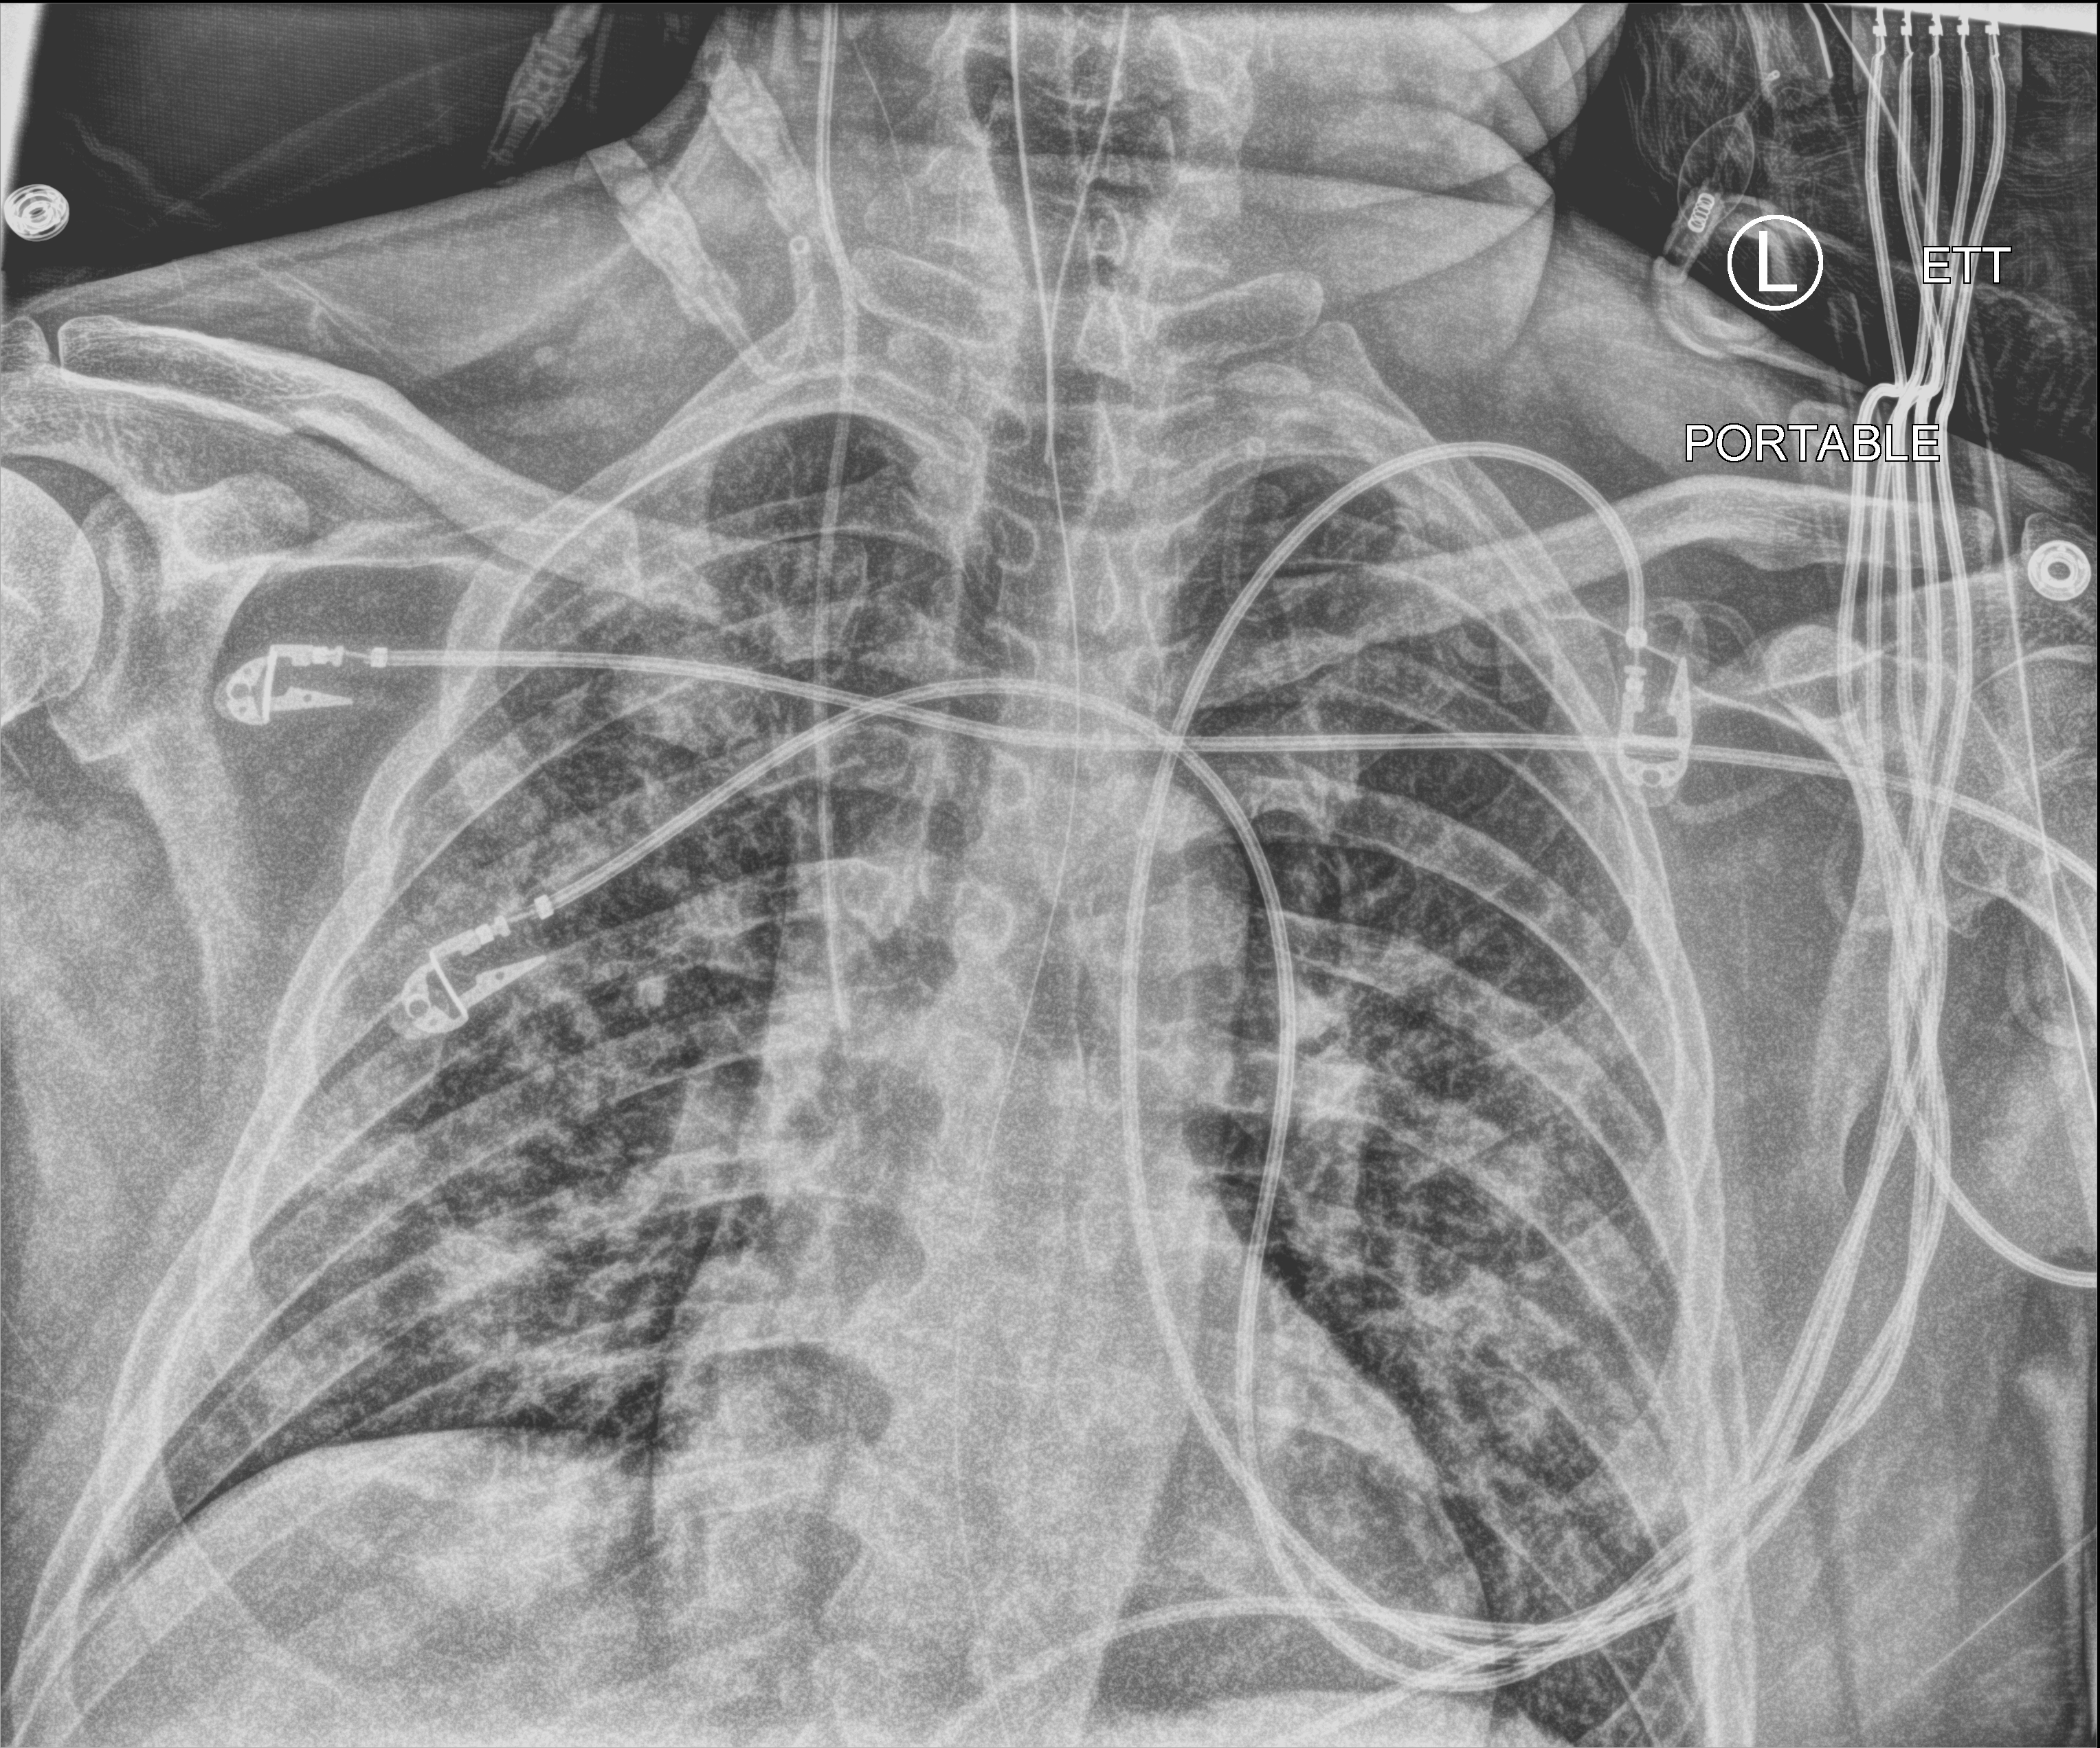
Bedside chest radiograph (computed radiography). Male patient hospitalised with COVID-19, age 18–59 years.
From the hospital-stay record, not from the radiograph (when in the stay this image was taken is not recorded): mechanically ventilated during this hospital stay: yes.